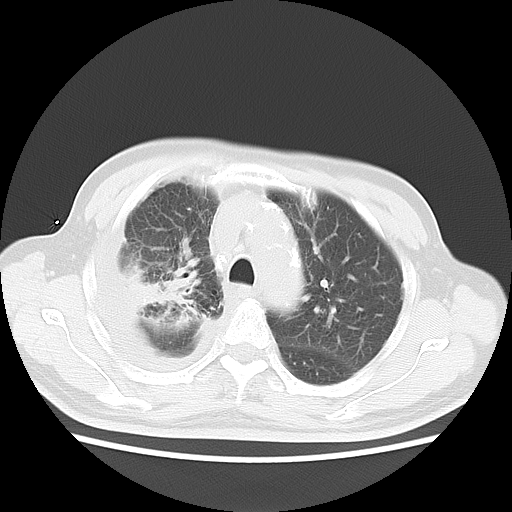
Chest CT, one axial slice. Position 11 of 20 along the scan axis. 120 kVp. Lung window (W 1500 / L -600 HU). 5 mm slice thickness. 512 × 512 image matrix, field of view 350 × 350 mm. Patient: male, 75 years. Case-level facts recorded for this patient, not image findings: clinical TNM (as recorded): T1c N1 M1.
Annotated regions visible in this slice (bounding box drawn by a radiologist):
- lung tumour (recorded histology: adenocarcinoma): bounding box <129,262,194,317> (left, top, right, bottom; pixels)